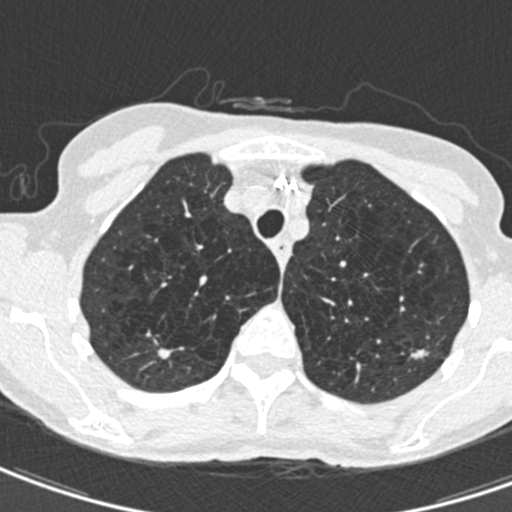
Low-dose screening chest CT, axial slice. Second screening round (one year after baseline). Lung window (W 1500 / L -600 HU). 0.75 mm slice thickness. Standard (soft-tissue) reconstruction kernel (B30f). Slice 109 of 498 in the series. 512 × 512 image matrix. Female, age 71 years at enrolment.
Expert reader's lesion annotation, bounding box (x1, y1, x2, y2) in pixels: (405, 332, 444, 370). The screening reader recorded 2 non-calcified nodules or masses ≥4 mm on this exam (right upper lobe, left upper lobe); which of them this box marks is not recorded. Official screen result: positive, change unspecified: nodule(s) >= 4 mm or enlarging nodule(s), mass(es), or other non-specific abnormalities suspicious for lung cancer. Lung cancer was diagnosed 604 days after this screen (after the third annual screen): adenocarcinoma, NOS, left upper lobe, moderately differentiated (G2), stage IA (AJCC 6th edition), 12 mm at pathology.